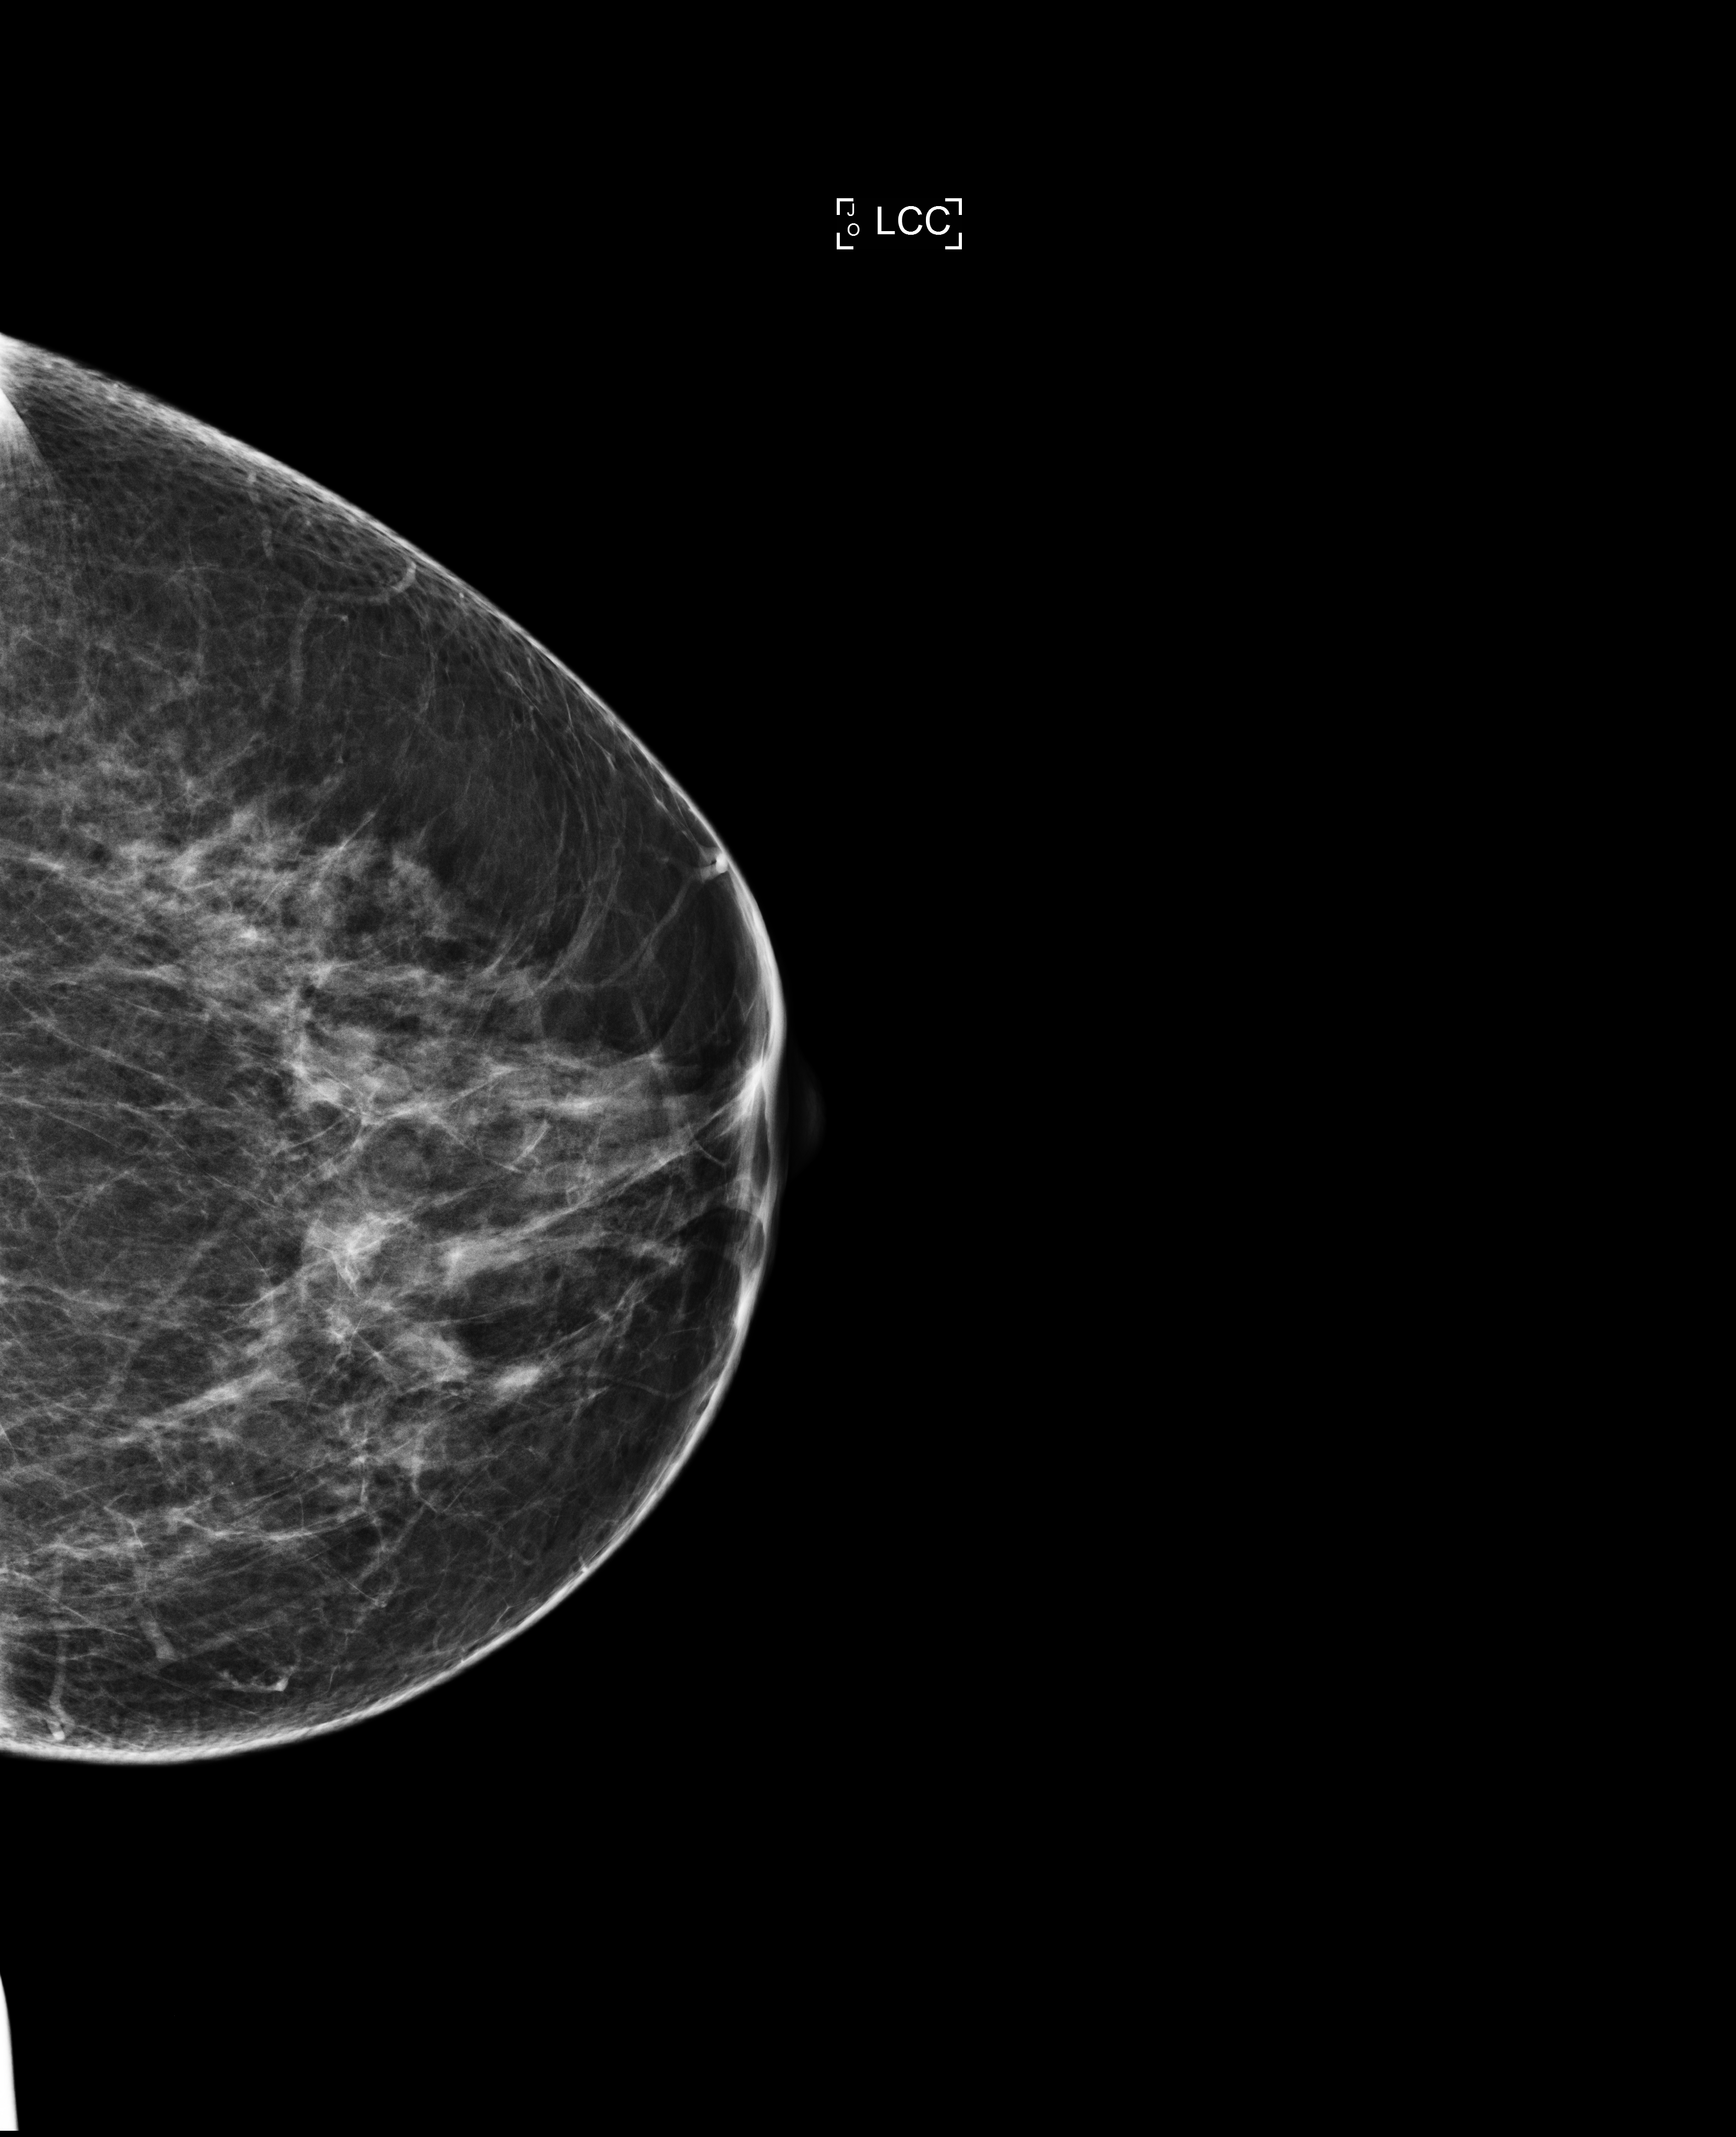
Annual screening mammography examination; compressed breast thickness 72 mm; system: Selenia Dimensions. Female patient, age 48 years.
Image type: full-field digital mammogram. Breast: left. Projection: CC view.